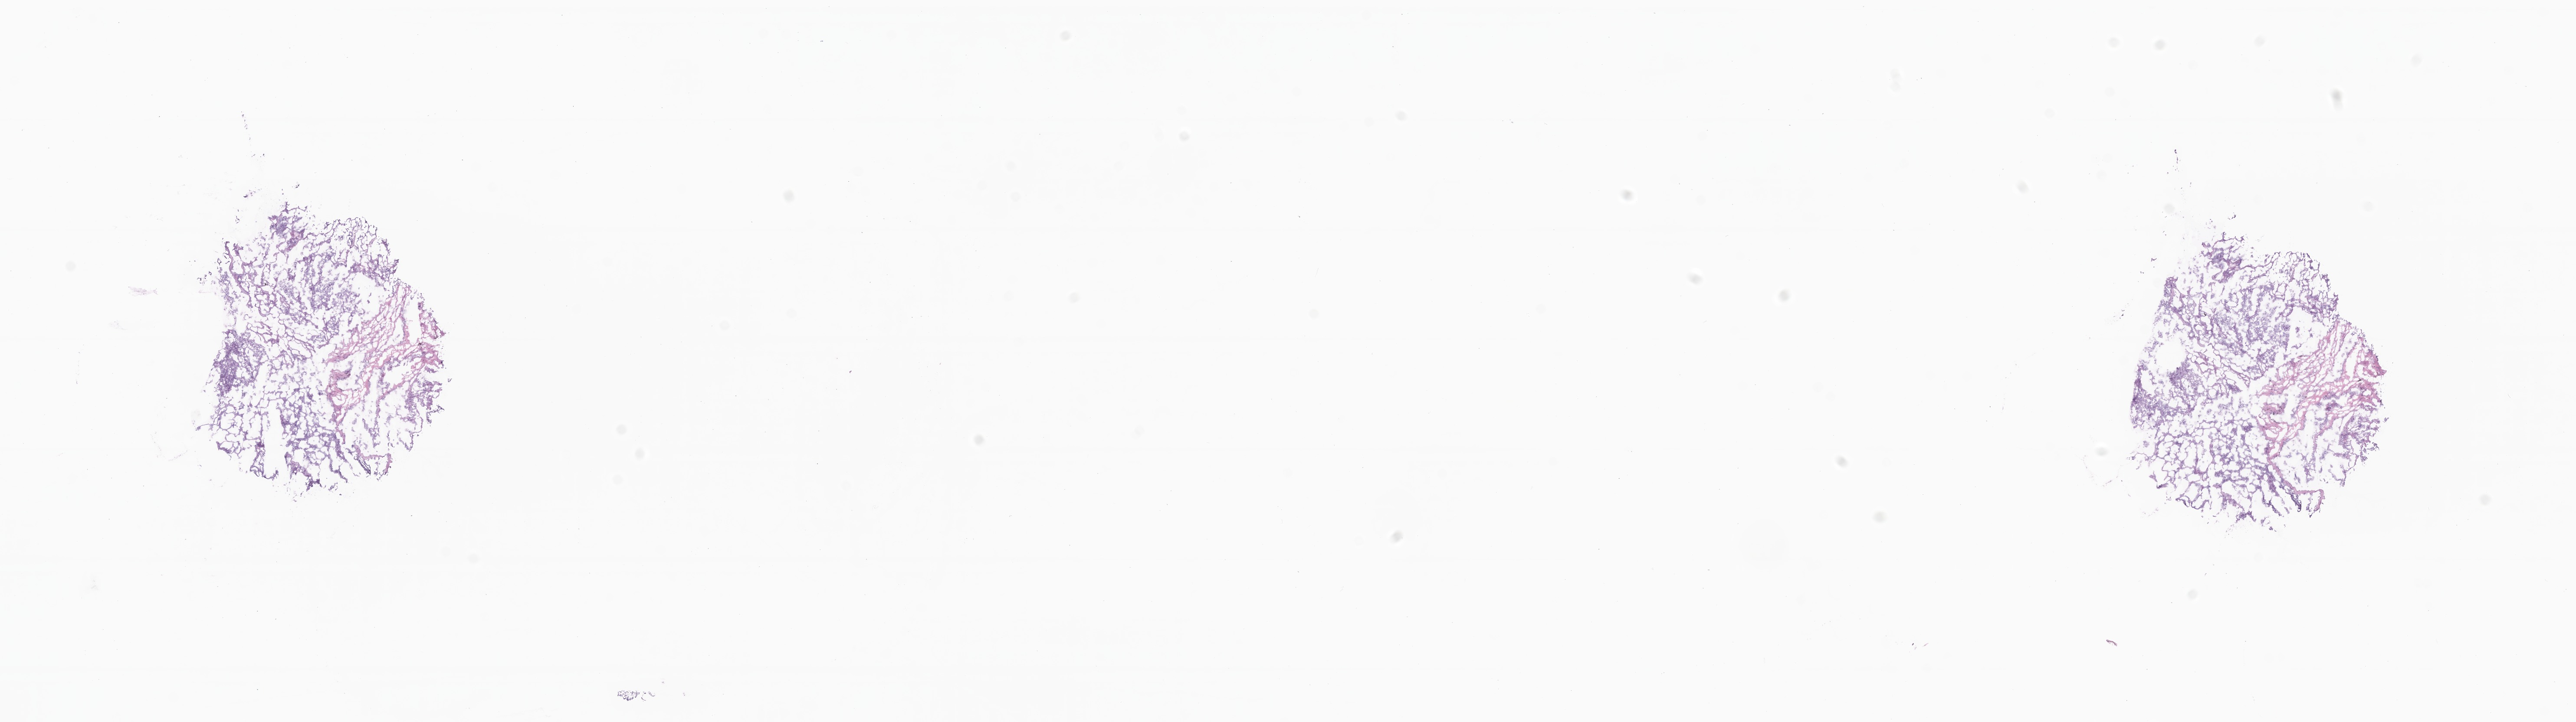
Whole-slide image, haematoxylin and eosin stain, low-resolution overview of the scanned area, about 25.0 x 7.0 mm; frozen section (tissue freezing medium); primary tumor; anatomic site: upper lobe of left lung. Patient: female, age at initial diagnosis 66 years. Tumor grade: G3 (poorly differentiated). Pathologist review of this section (percent, as recorded): tumor cells 80%, tumor nuclei 80%, stromal cells 17%, necrosis 1%, normal cells 2%. Infiltration values recorded for this section: lymphocyte infiltration 5%, monocyte infiltration 3%, neutrophil infiltration 4%.
- diagnosis: Adenocarcinoma, NOS
- AJCC pathologic stage: Stage IB